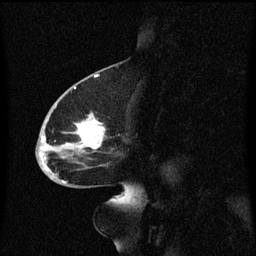
Breast MRI (dynamic contrast-enhanced), one sagittal slice; slice 30 of 60 in the series (ordered by position); dynamic contrast-enhanced series, image 2 of 3 at this slice position (ordered by acquisition); 1.5 T; TE 4.2 ms, TR 8.4 ms; 2 mm slice thickness; 256 × 256 image matrix, field of view 200 × 200 mm. Female patient, age 68 years. From the clinical record (not read from this slice): setting: breast cancer imaged before/during neoadjuvant chemotherapy; receptor status: triple-negative.
Structures marked on this image (semi-automatically segmented with operator editing):
- analysis volume of interest (the breast-tissue region the enhancement analysis was run in; not a lesion): bounding box [x1, y1, x2, y2] px = [37, 94, 108, 173]
- tumour enhancement mask (voxels above the 70 % enhancement threshold inside the analysis volume of interest): [41, 116, 106, 171]